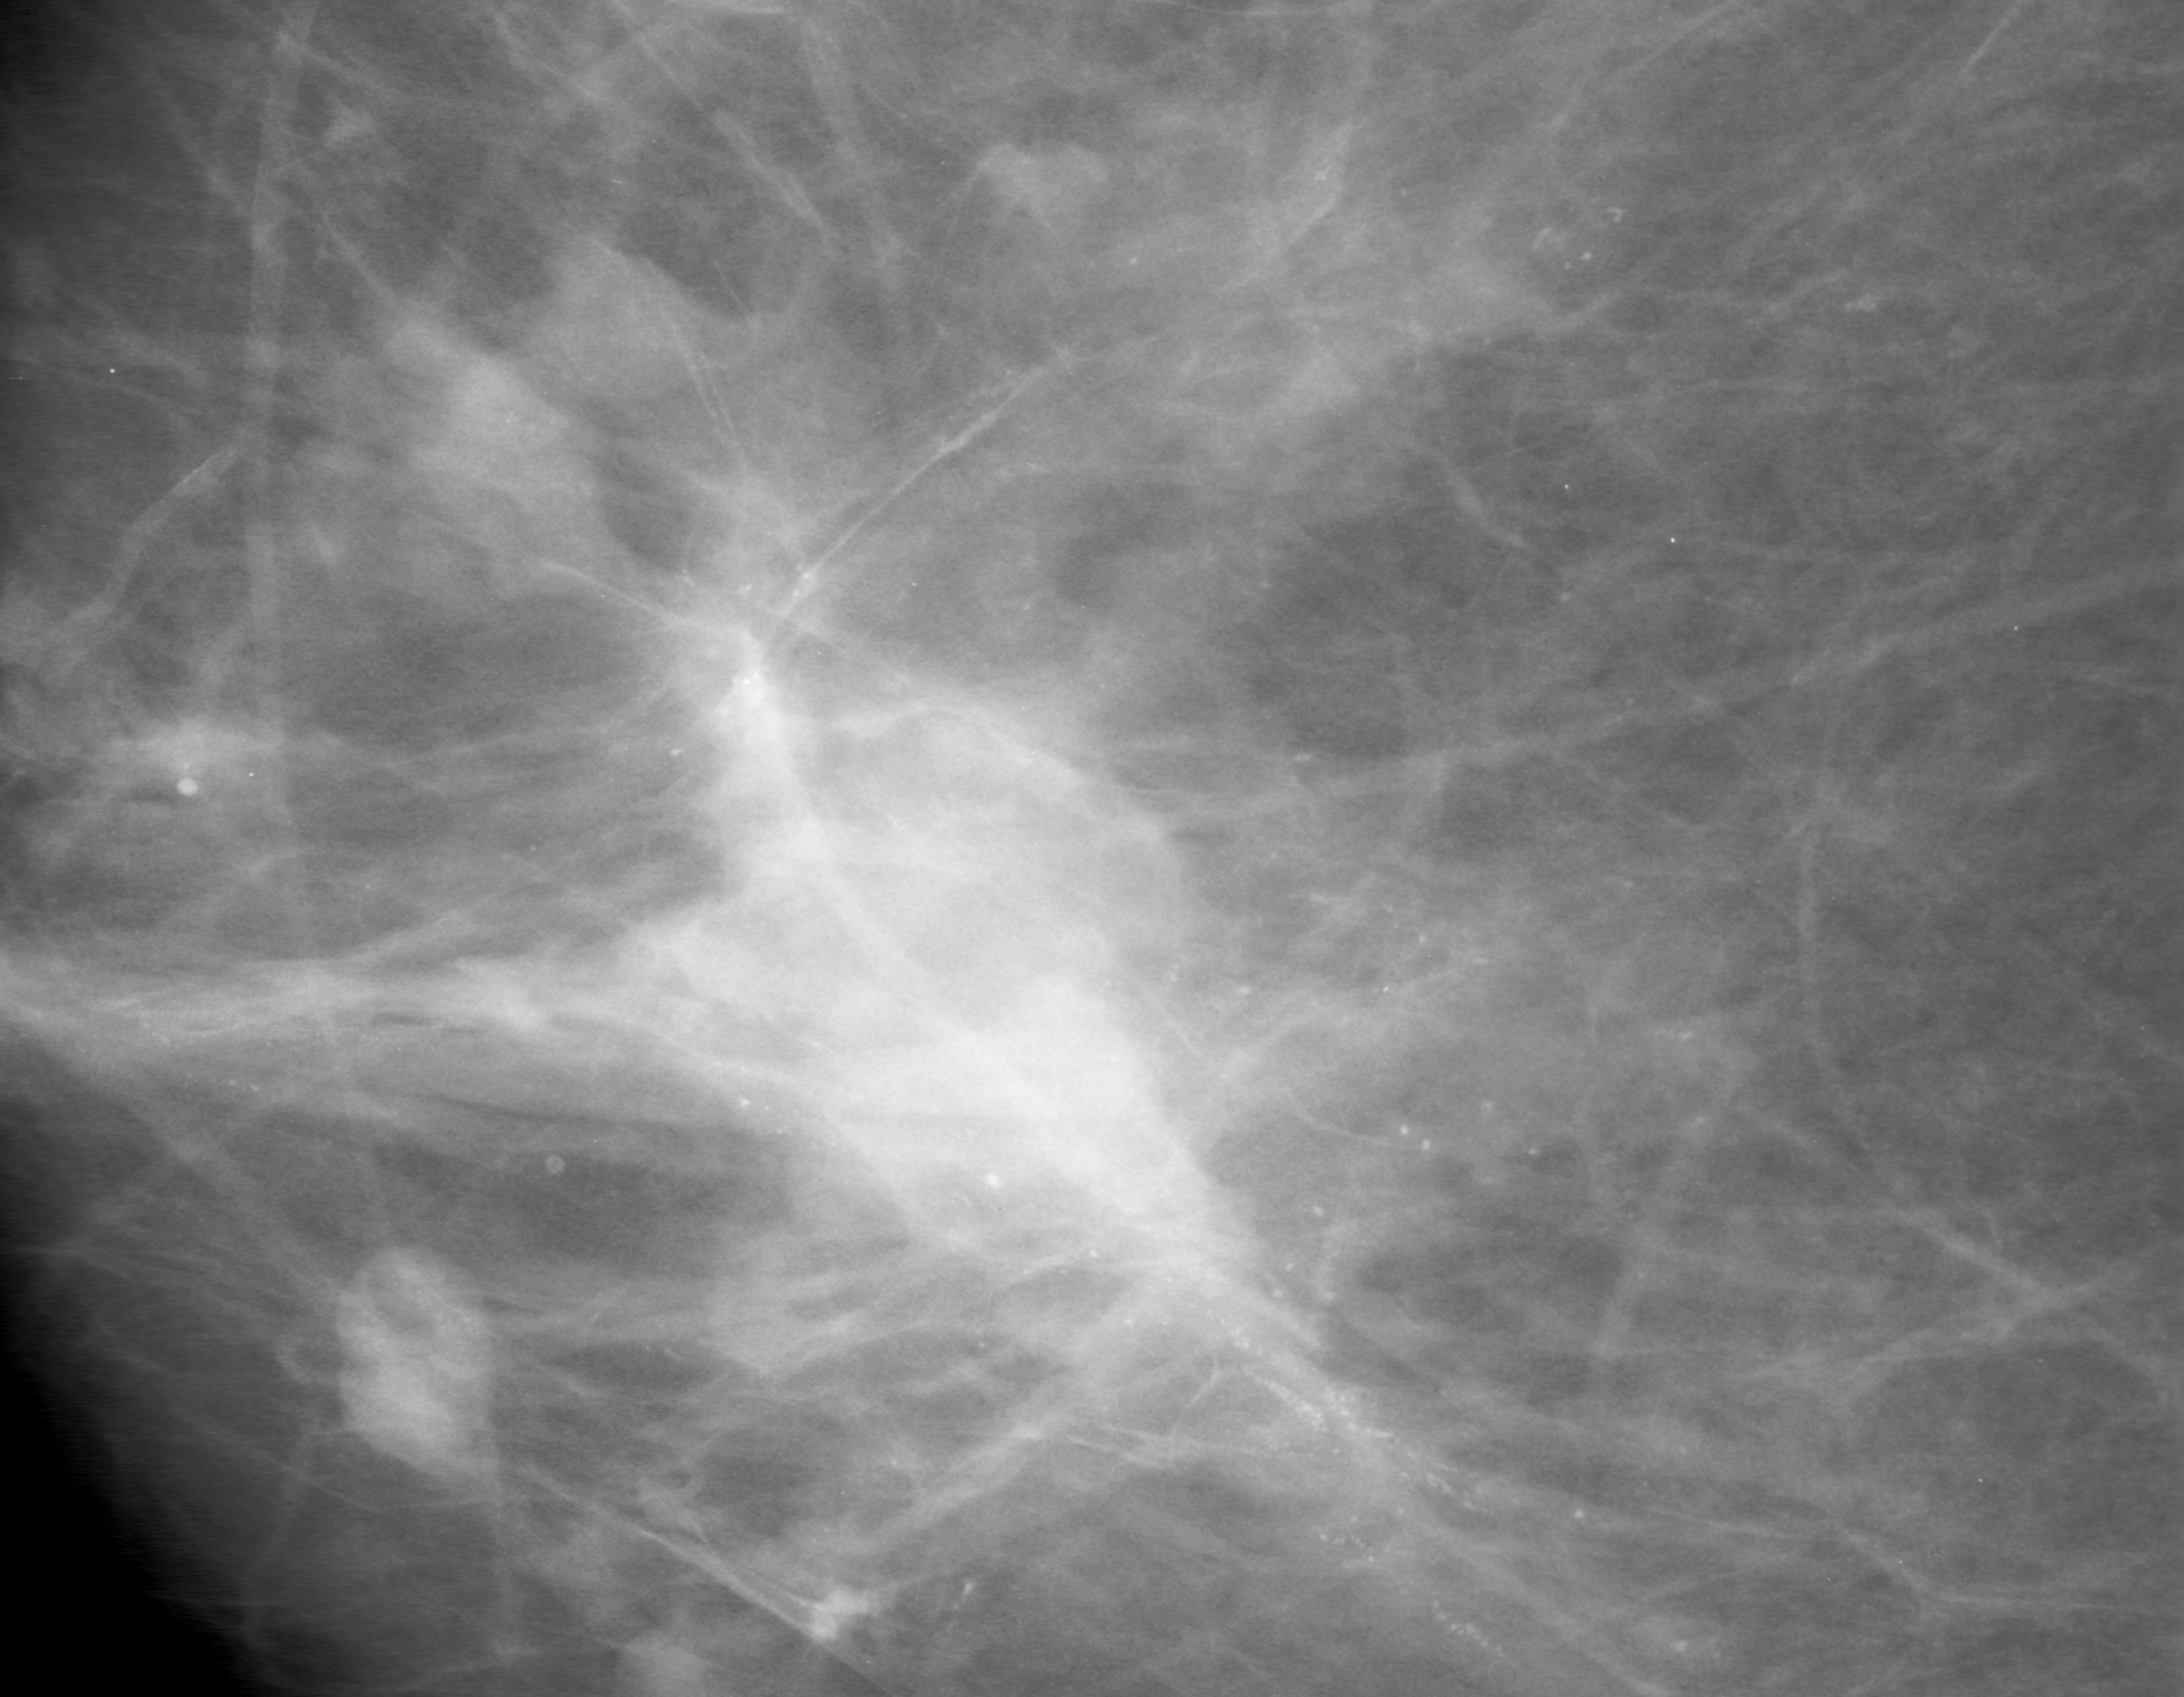
Crop from a digitized film mammogram around one marked abnormality, right breast, CC view.
Finding: calcifications, morphology amorphous / pleomorphic, distribution segmental; BI-RADS assessment category 5; pathology result (as recorded, not read from the image): malignant.